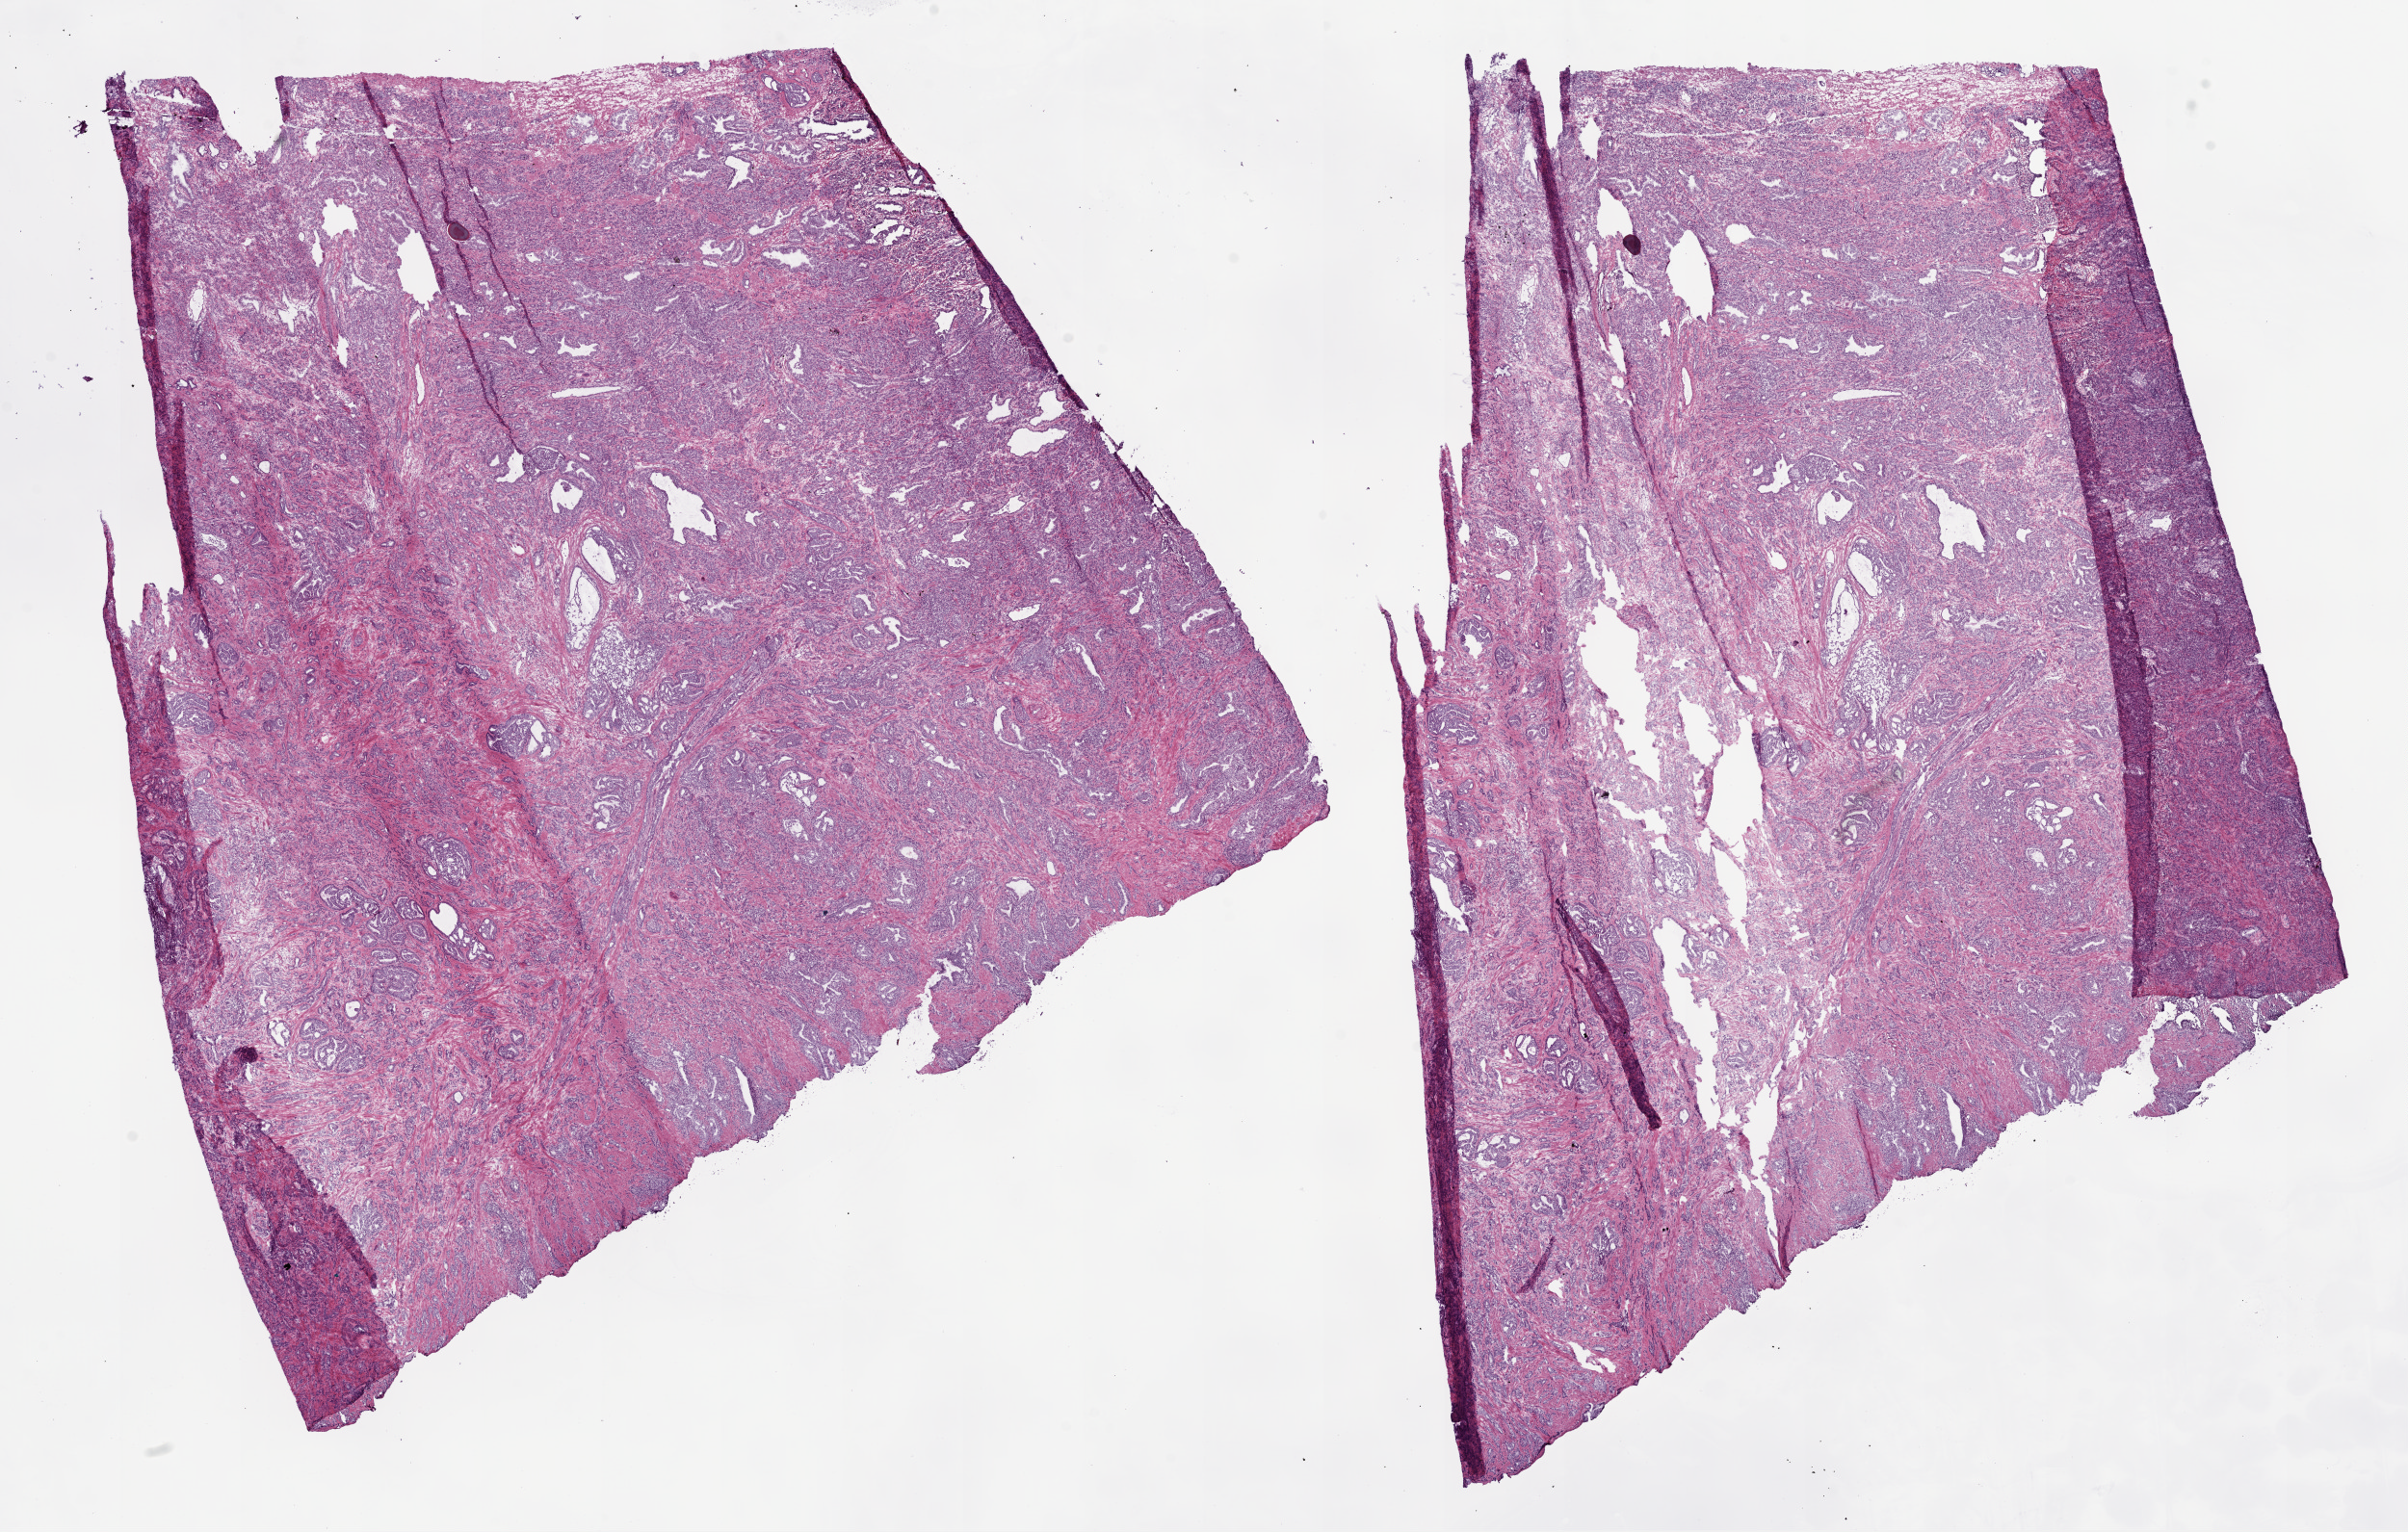
H&E whole-slide image — a low-resolution overview of the entire scanned area, about 20.1 x 12.8 mm (from a 20x scan), frozen section from the top of the tissue portion, prostate, primary tumour sample. Patient: male, age at initial diagnosis 67 years. Gleason score: 8 (5+3). Composition of this section per pathologist review: tumour cells 70%, tumour nuclei 80%, normal cells 10%, stromal cells 20%, necrosis 0%. Infiltration values recorded for this section: lymphocyte infiltration 2%, monocyte infiltration 0%, neutrophil infiltration 0%.
Pathologic diagnosis: Acinar cell carcinoma (prostate gland).